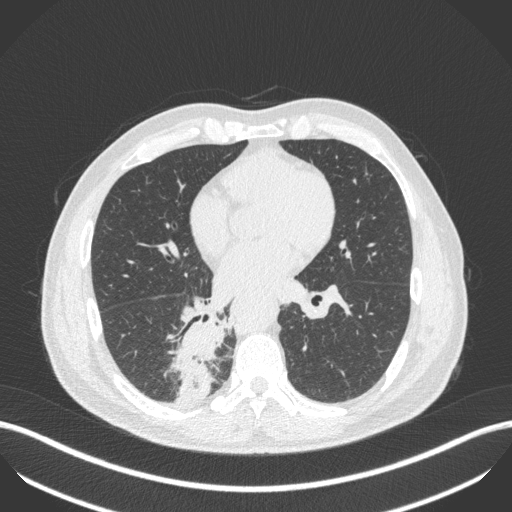
Chest CT, one axial slice; slice 219 of 451 in the series (ordered by position); reconstruction kernel B31f; 100 kVp; lung window (W 1500 / L -600 HU); 1 mm slice thickness; 512 × 512 image matrix, field of view 400 × 400 mm. Male patient, age 61 years. From the clinical record (not read from this slice): clinical TNM (as recorded): T1 N0 M0; histopathological grade: G3.
Structures marked on this image (rectangle marked by the reading radiologist):
- lung tumour (recorded histology: small cell carcinoma): bounding box <172,315,225,409> (left, top, right, bottom; pixels)